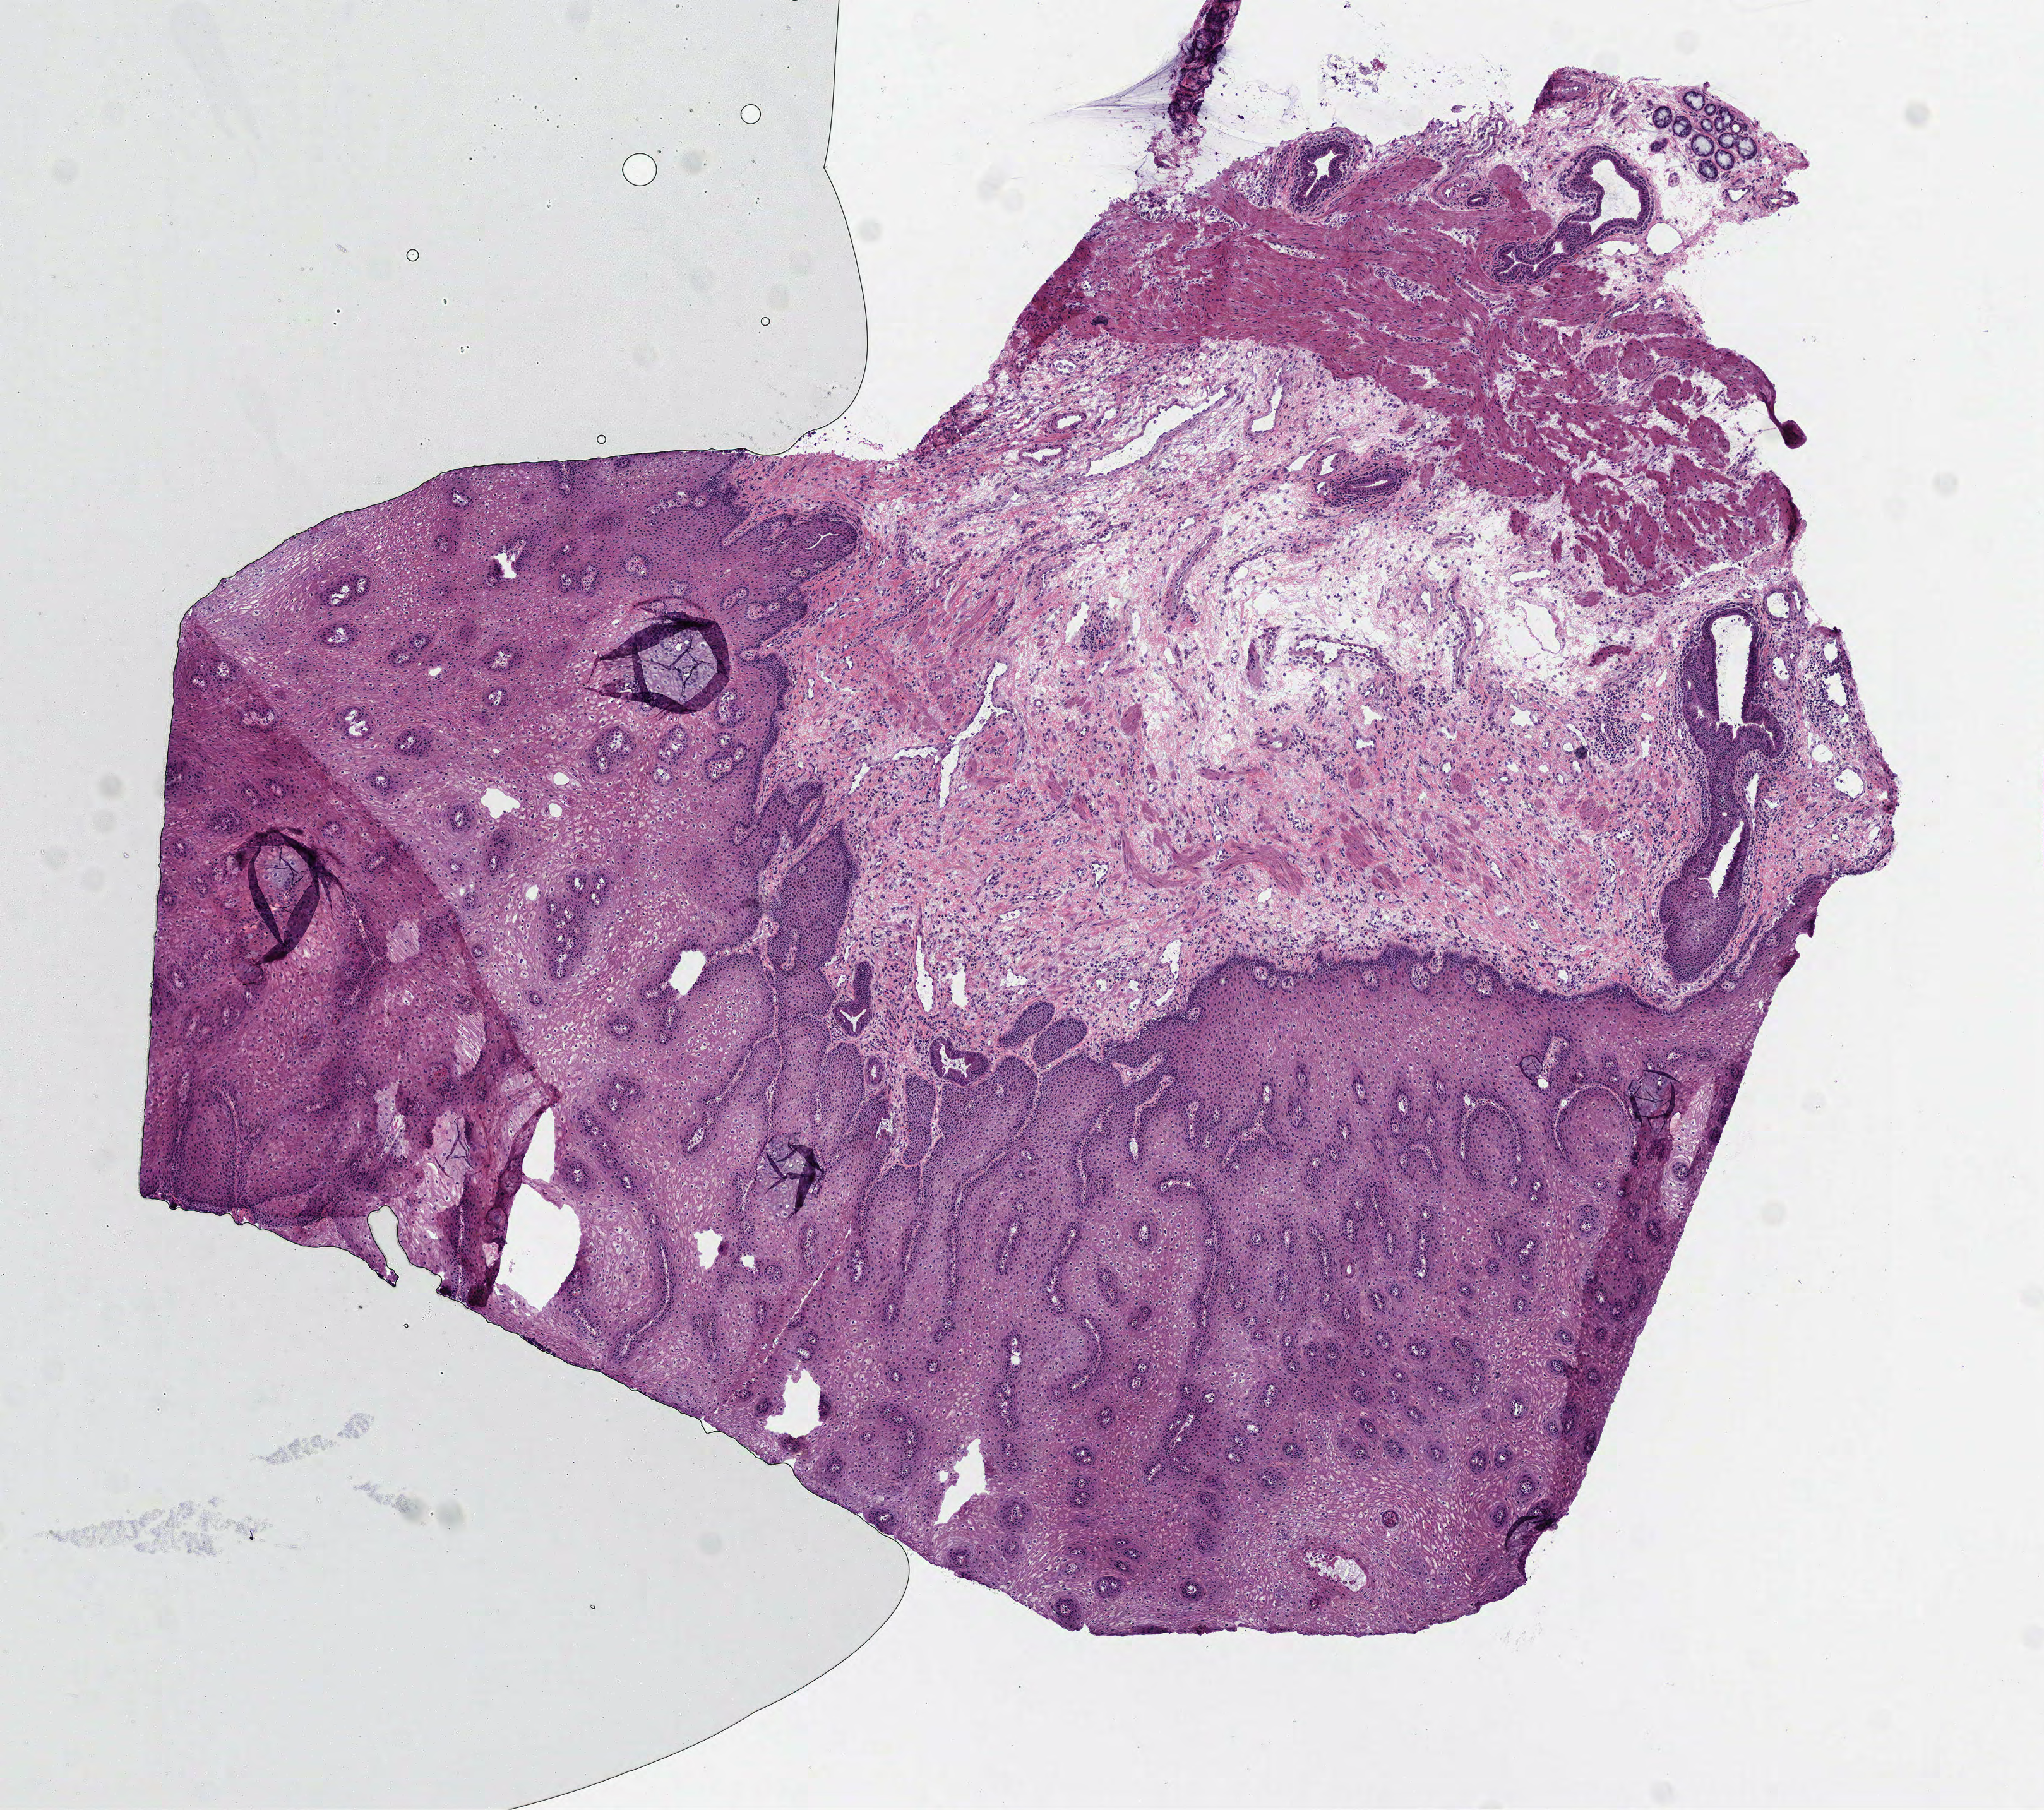
H&E whole-slide image, a low-resolution overview of the entire scanned area, about 6.5 x 5.8 mm (acquisition: 40x scan), frozen section from the top of the tissue portion, solid tissue normal (non-tumour tissue) sample from the stomach. Male patient; age at initial diagnosis 74 years. Infiltration values recorded for this section: lymphocyte infiltration 2%, monocyte infiltration 0%, neutrophil infiltration 0%.
- this section: solid tissue normal sample (biorepository sample class)
- patient diagnosis: Signet ring cell carcinoma (cardia, NOS)